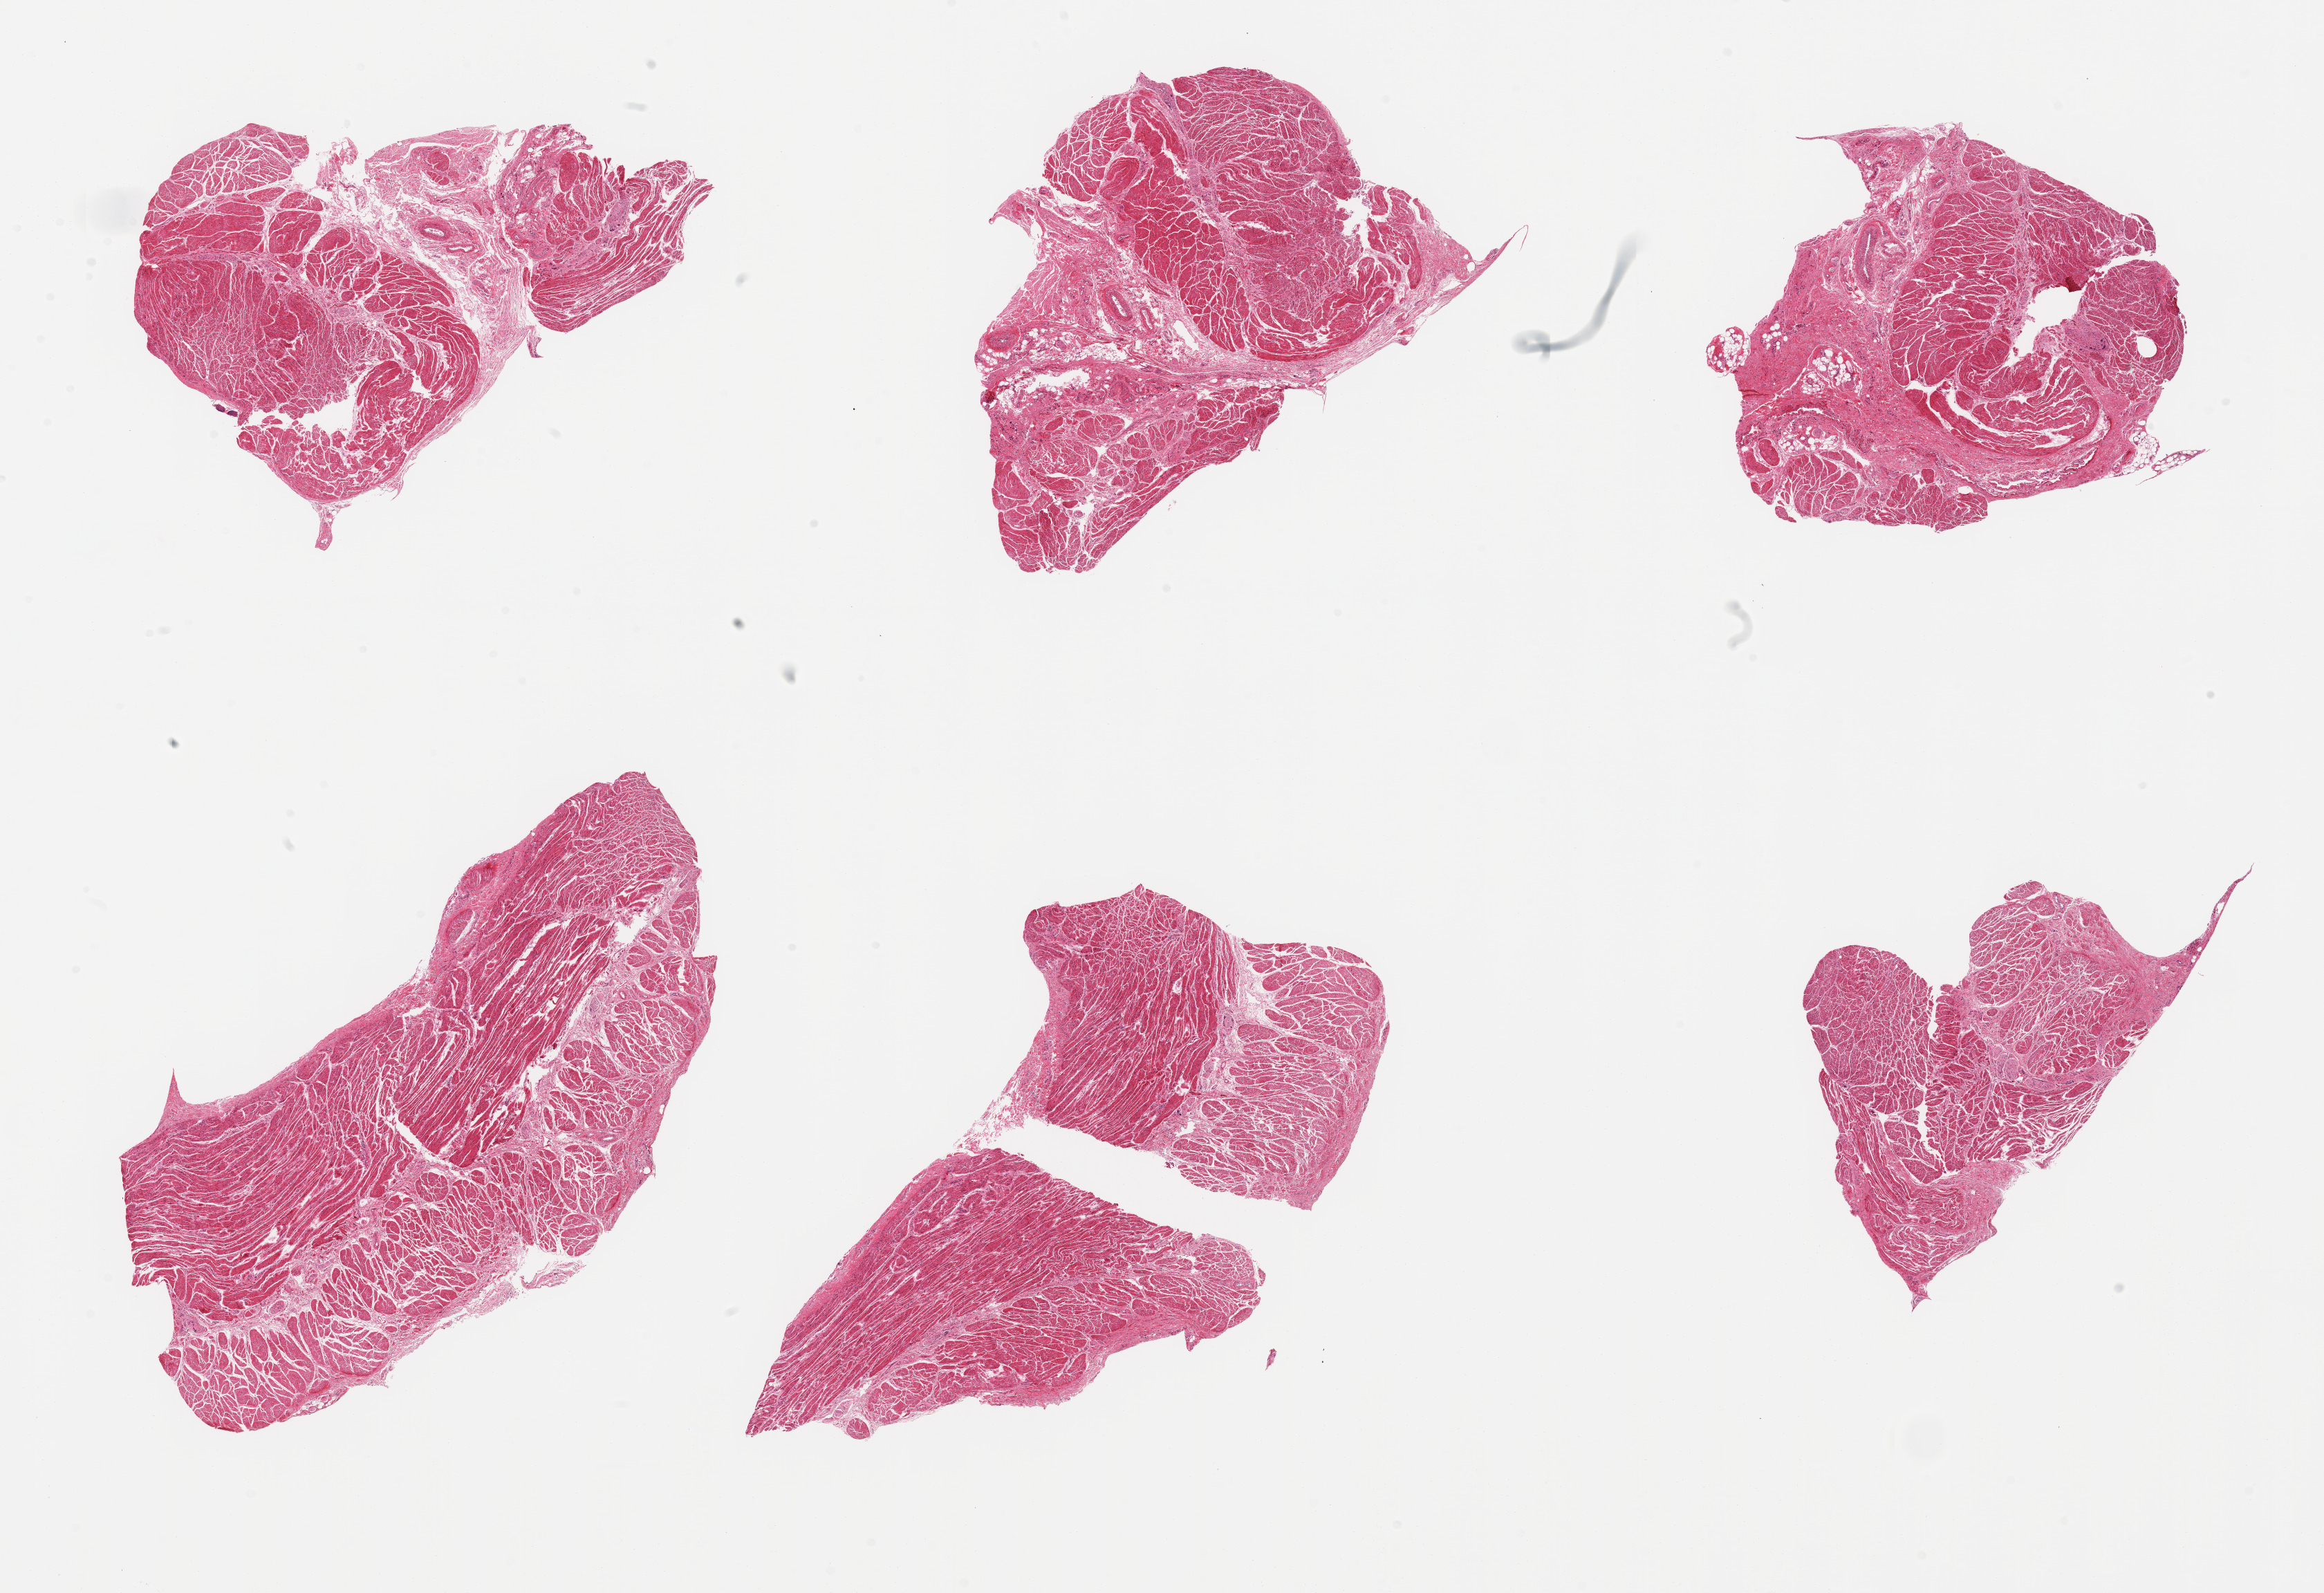
Digitized H&E-stained section, shown as a low-resolution overview of the whole scanned area (about 26.6 x 18.2 mm, slide scanned at 20x); PAXgene-fixed paraffin-embedded (PFPE) section; target tissue: gastroesophageal junction; donor tissue sample. Male donor.
Review note (as recorded): 6 pieces, confirmed target muscularis.